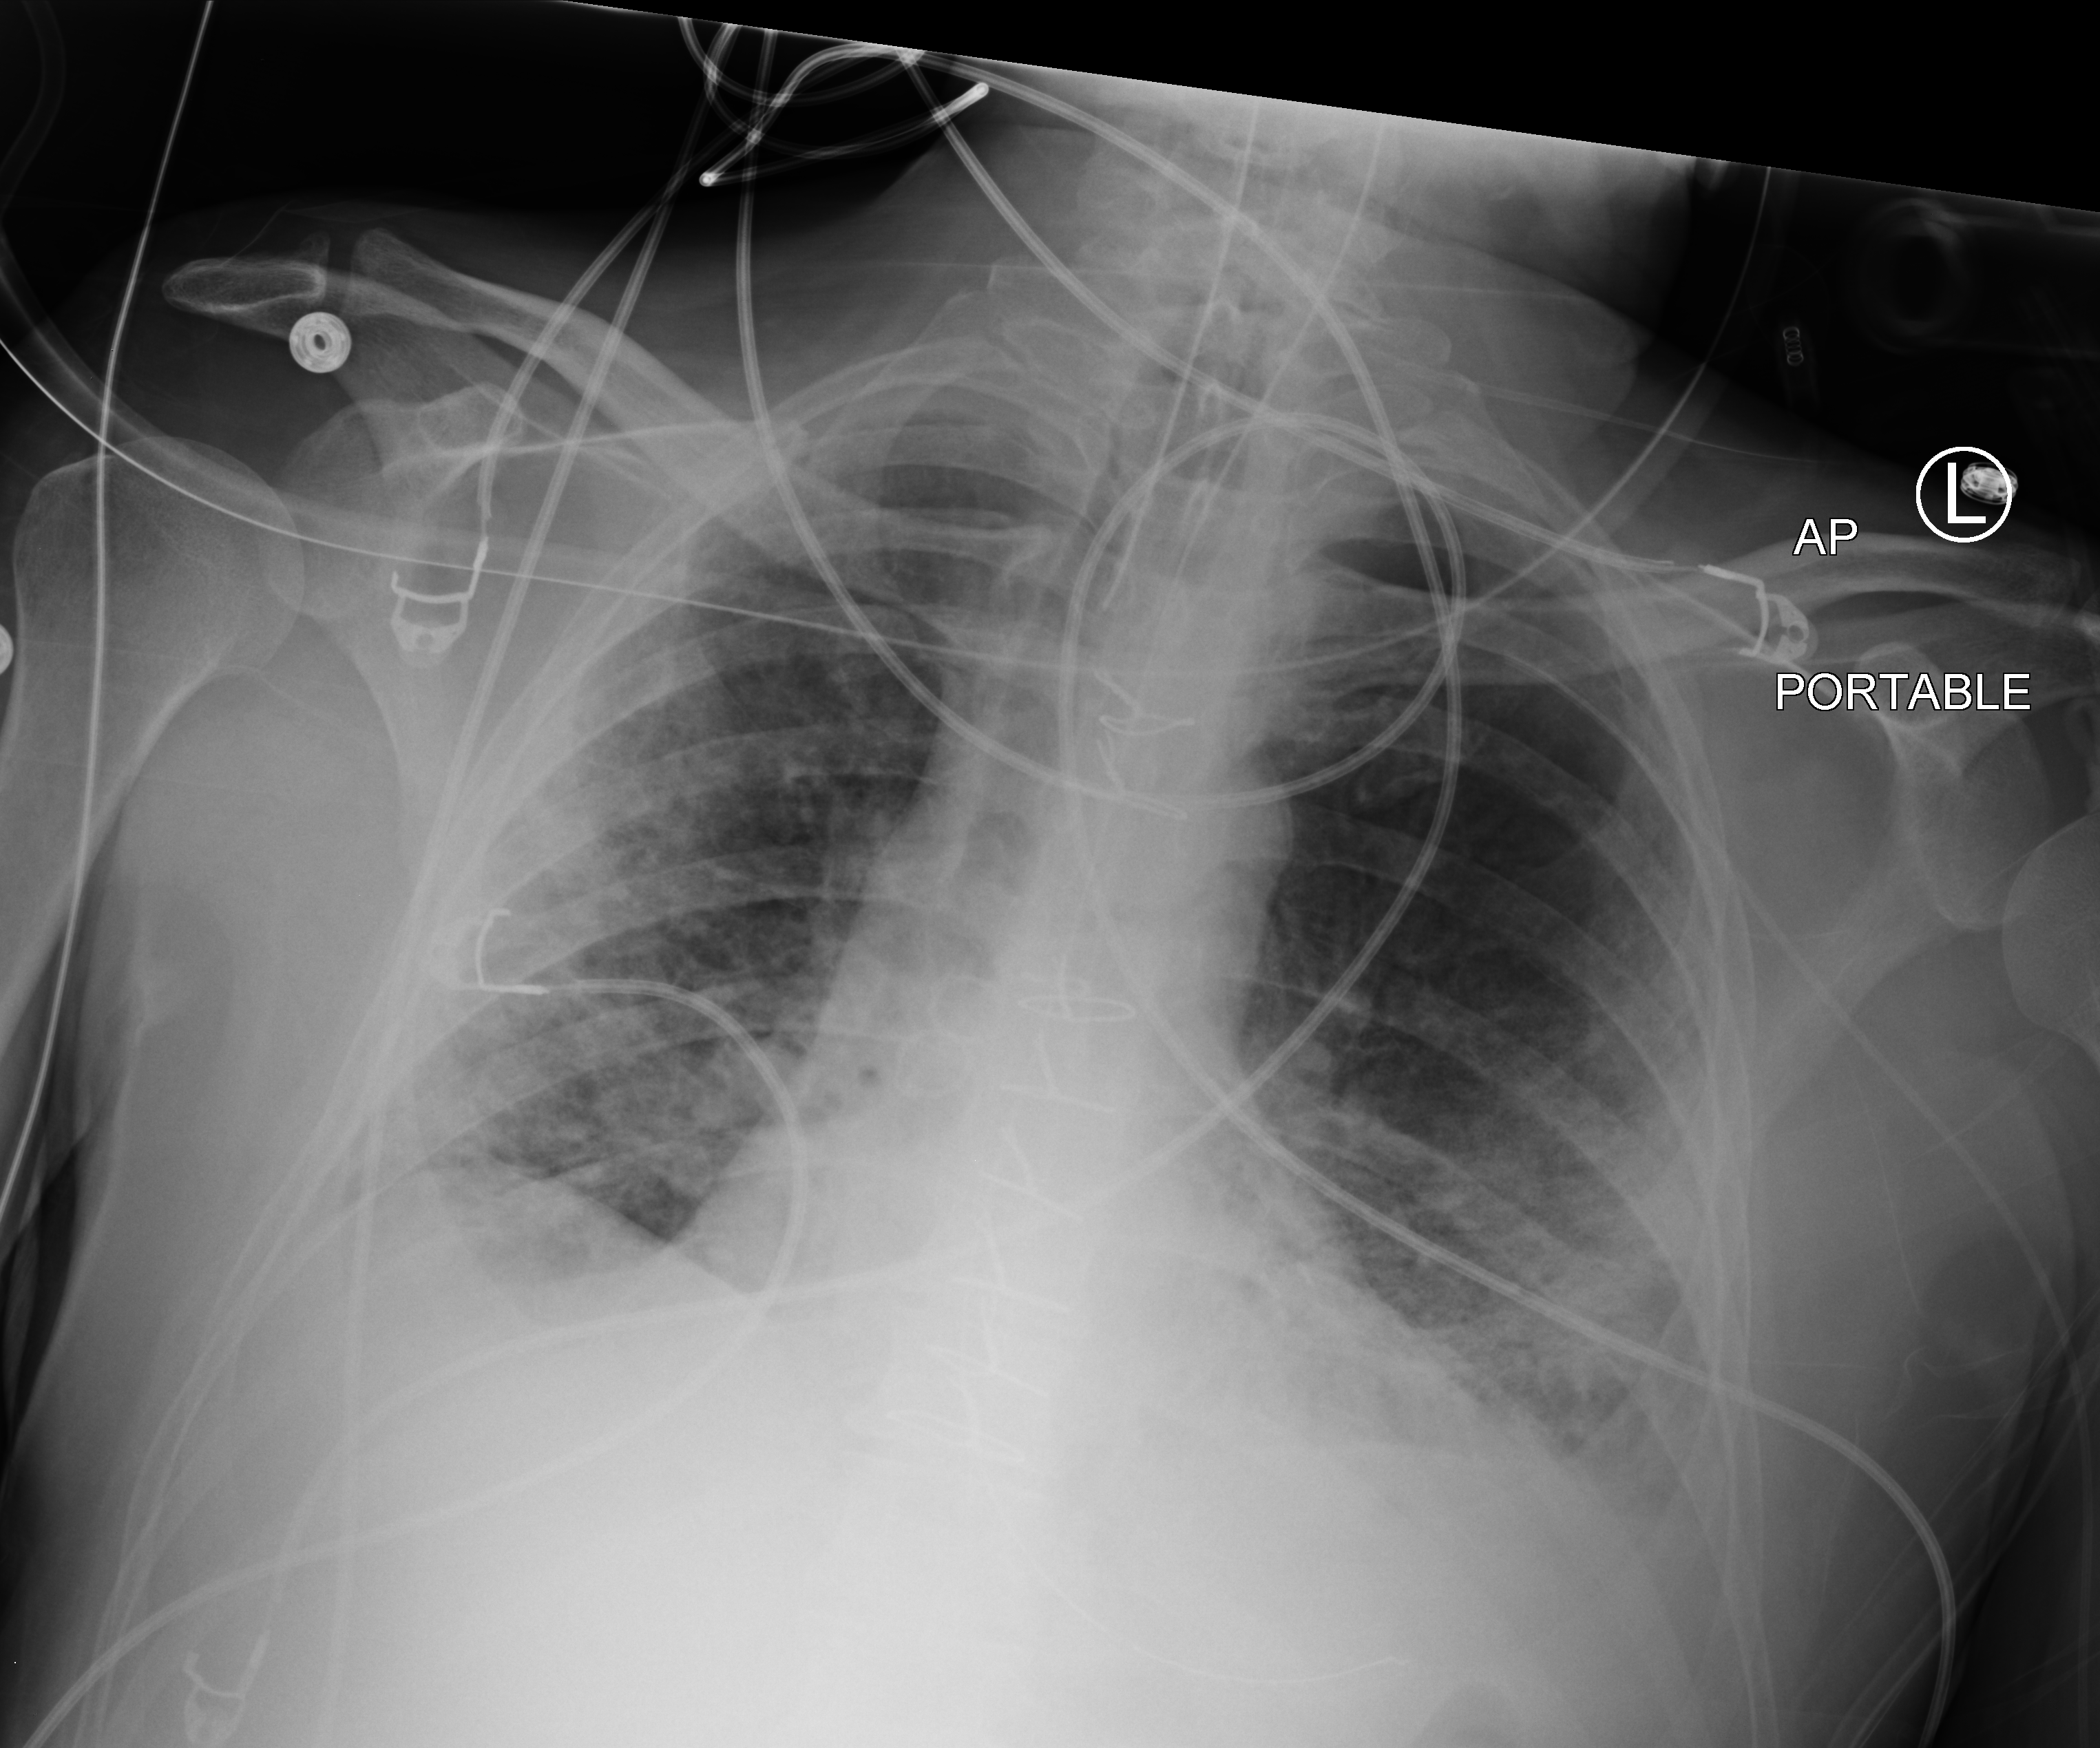
Bedside chest radiograph (computed radiography); anteroposterior (AP) projection. Male patient hospitalised with COVID-19, age 18–59 years.
Hospital-stay facts (about this admission, not read from this image; timing relative to this image not recorded):
- admitted to intensive care during this hospital stay: yes
- mechanically ventilated during this hospital stay: yes
- smoking status (admission record): former